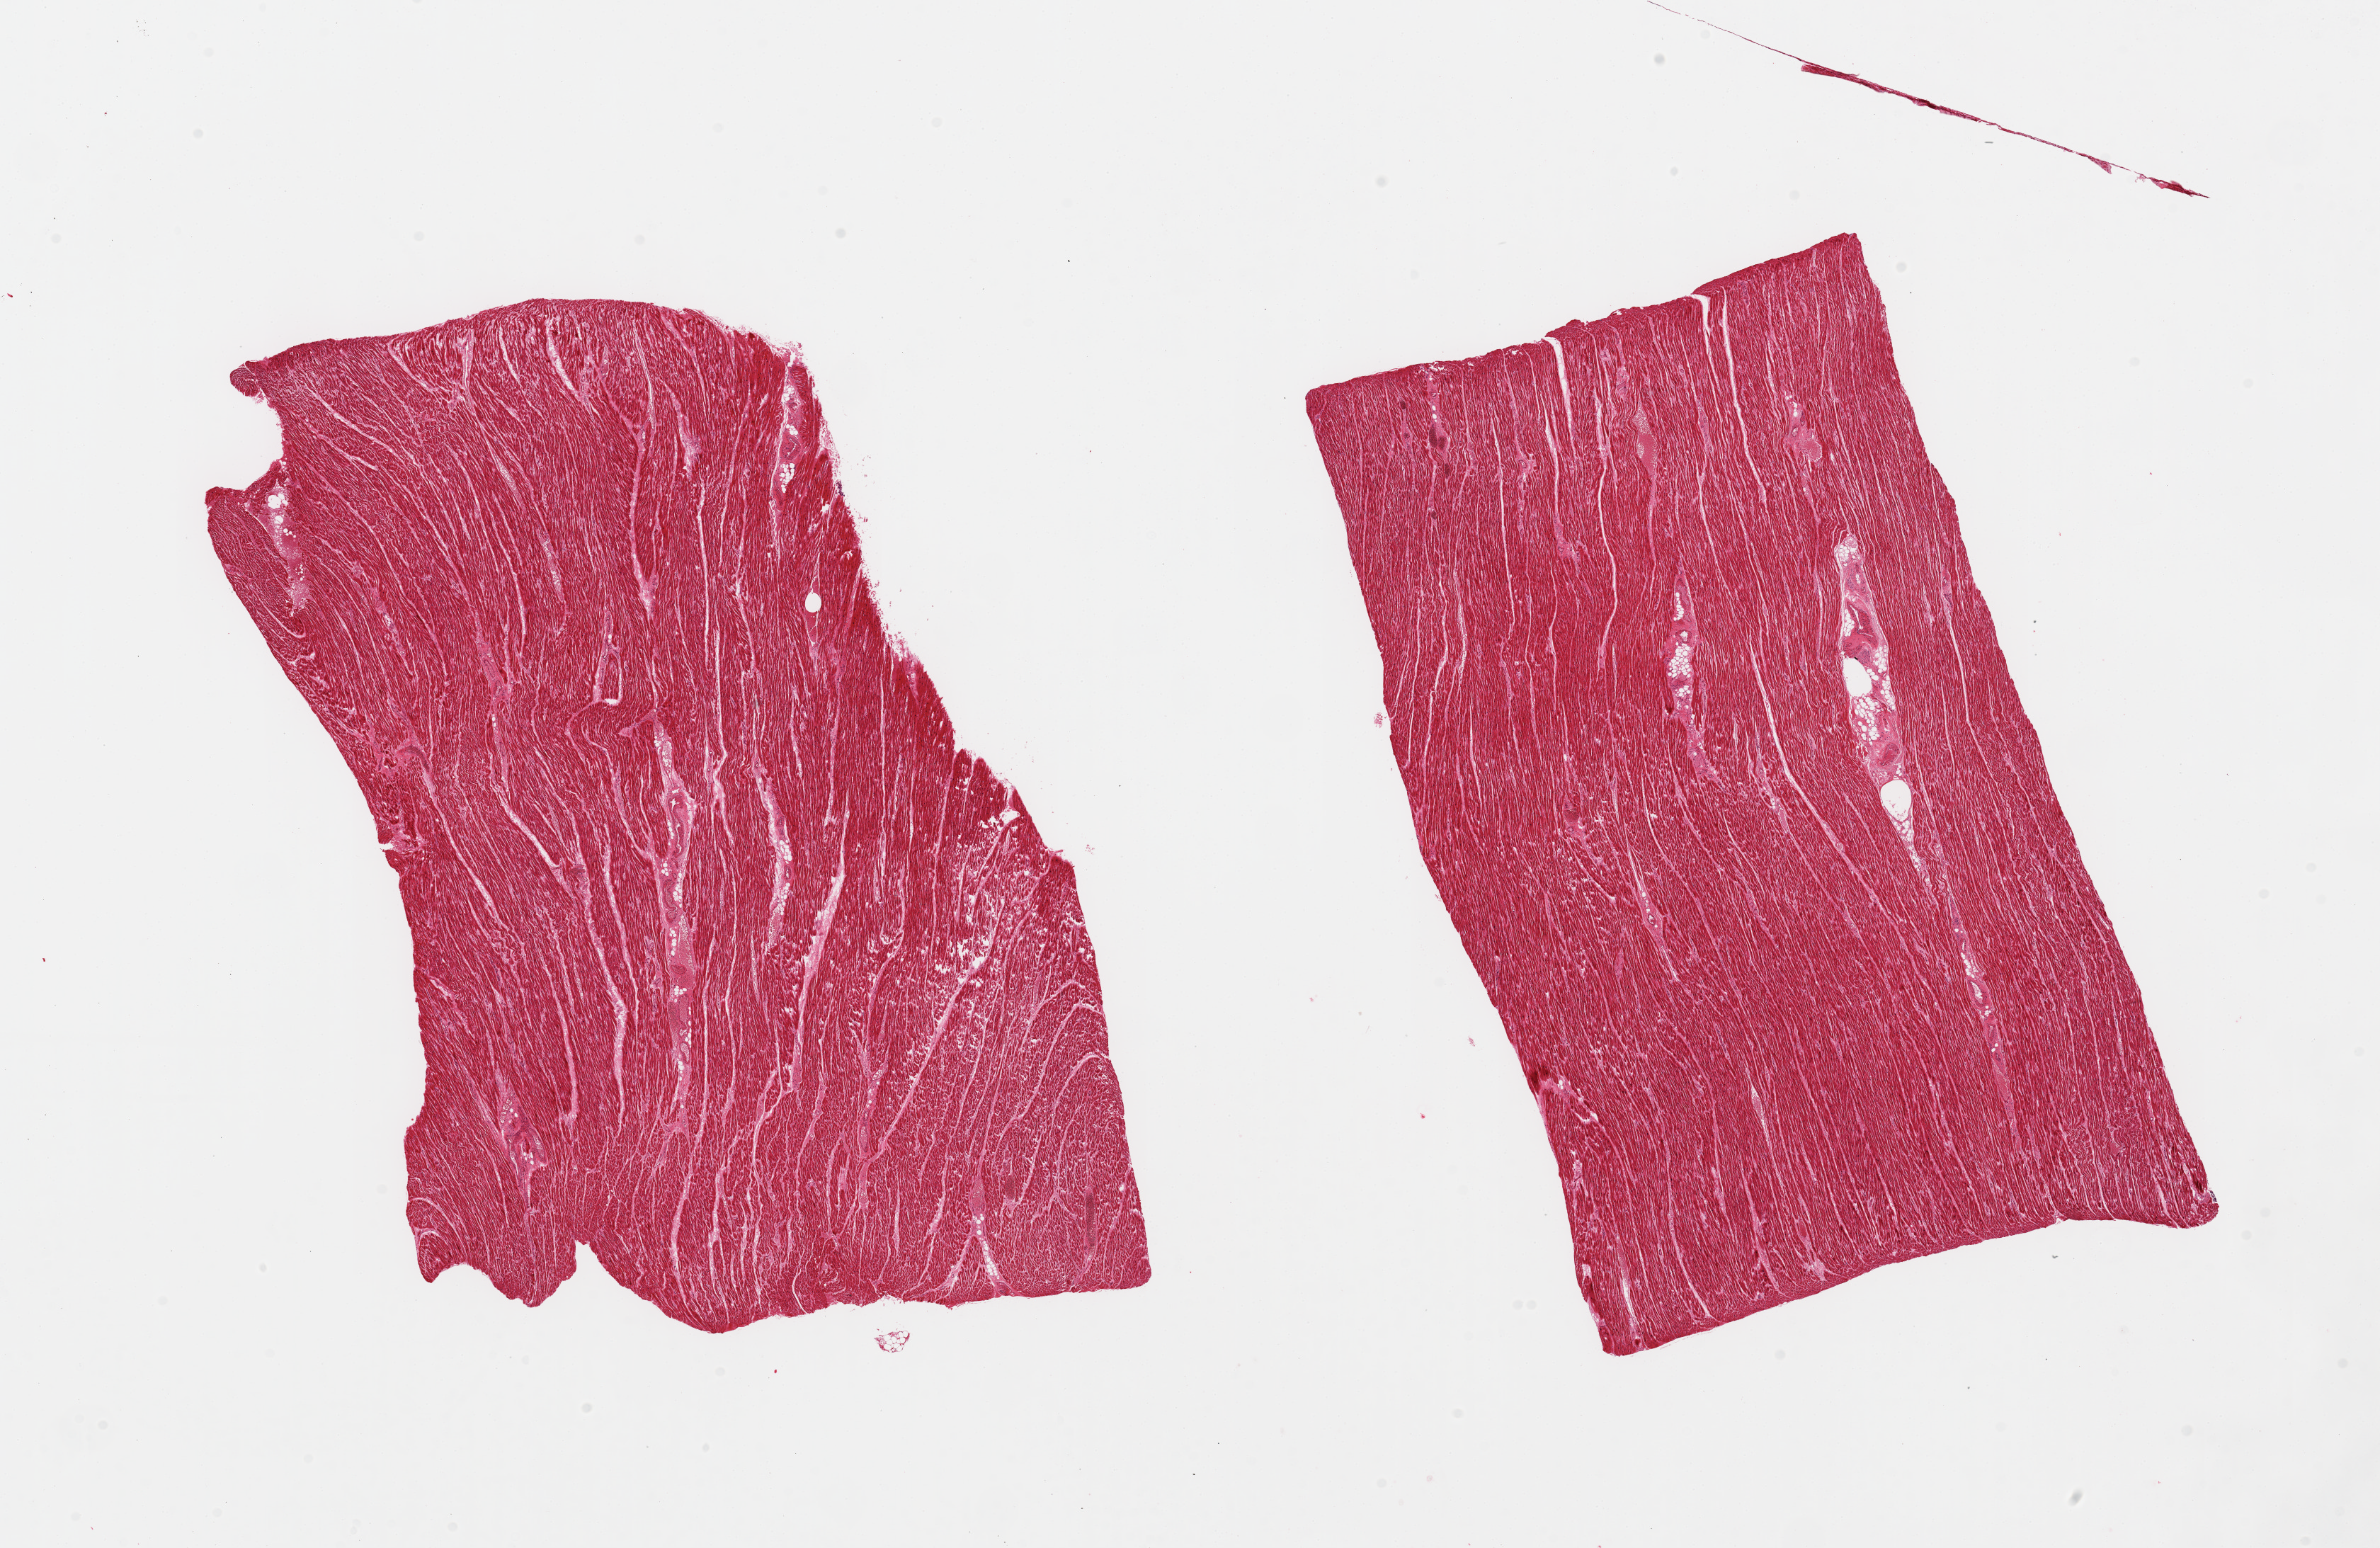
Hematoxylin and eosin (H&E) whole-slide image, whole scanned area (about 26.6 x 17.3 mm) shown as a low-resolution overview, PAXgene-fixed paraffin-embedded (PFPE) section, sampled site (target tissue): heart, tissue donor sample. Donor sex: male.
Pathologist's review note for this sample: 2 pieces.